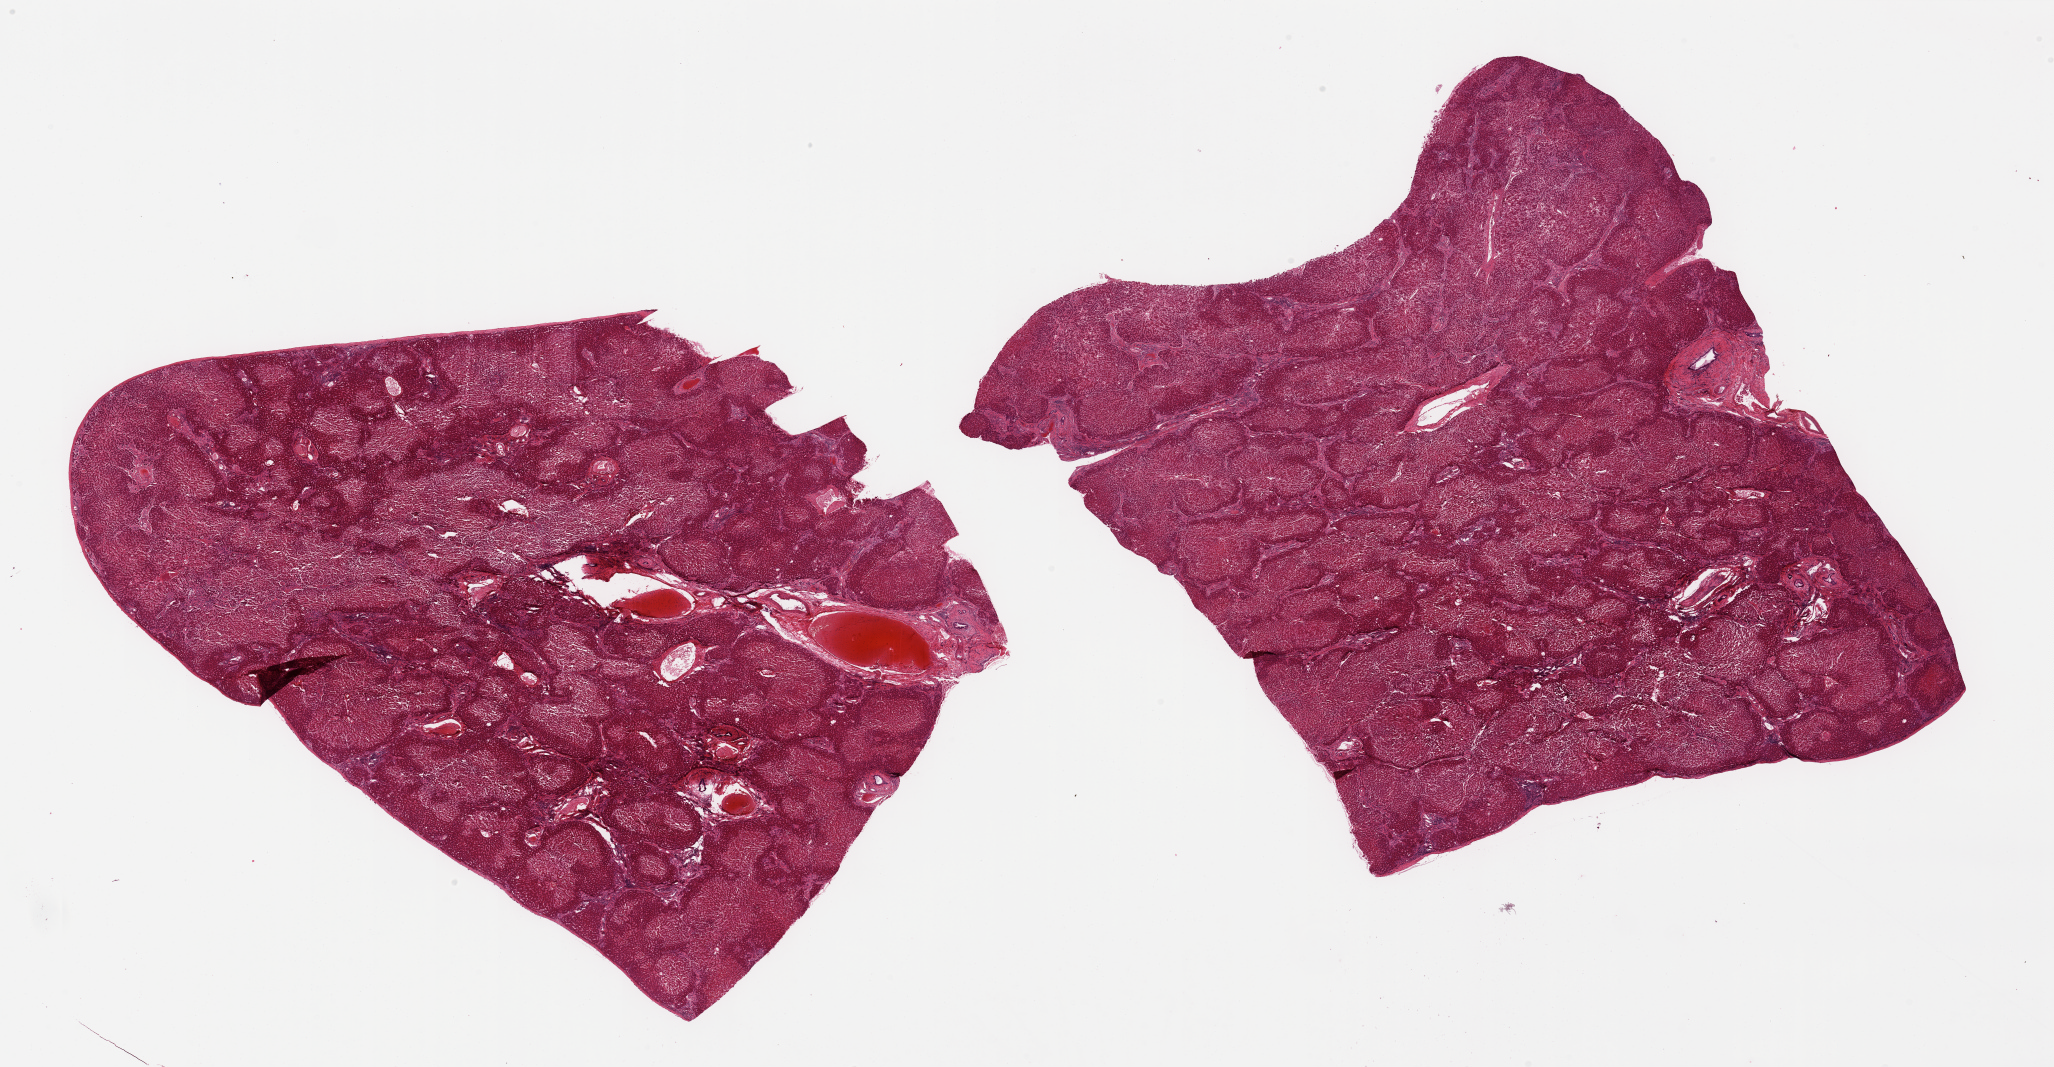
Haematoxylin and eosin whole-slide image — shown as a low-resolution overview of the whole scanned area (about 32.5 x 16.9 mm, from a 20x scan); PAXgene-fixed paraffin-embedded (PFPE) section; section of liver (target tissue); tissue donor sample.
Review note (as recorded): 2 pieces; includes capsule (target is 1cm below capsule), bridging fibrosis with expanded portal tracks and lymphocytic infiltrate, history of sclerosis cholangitis, congestion.